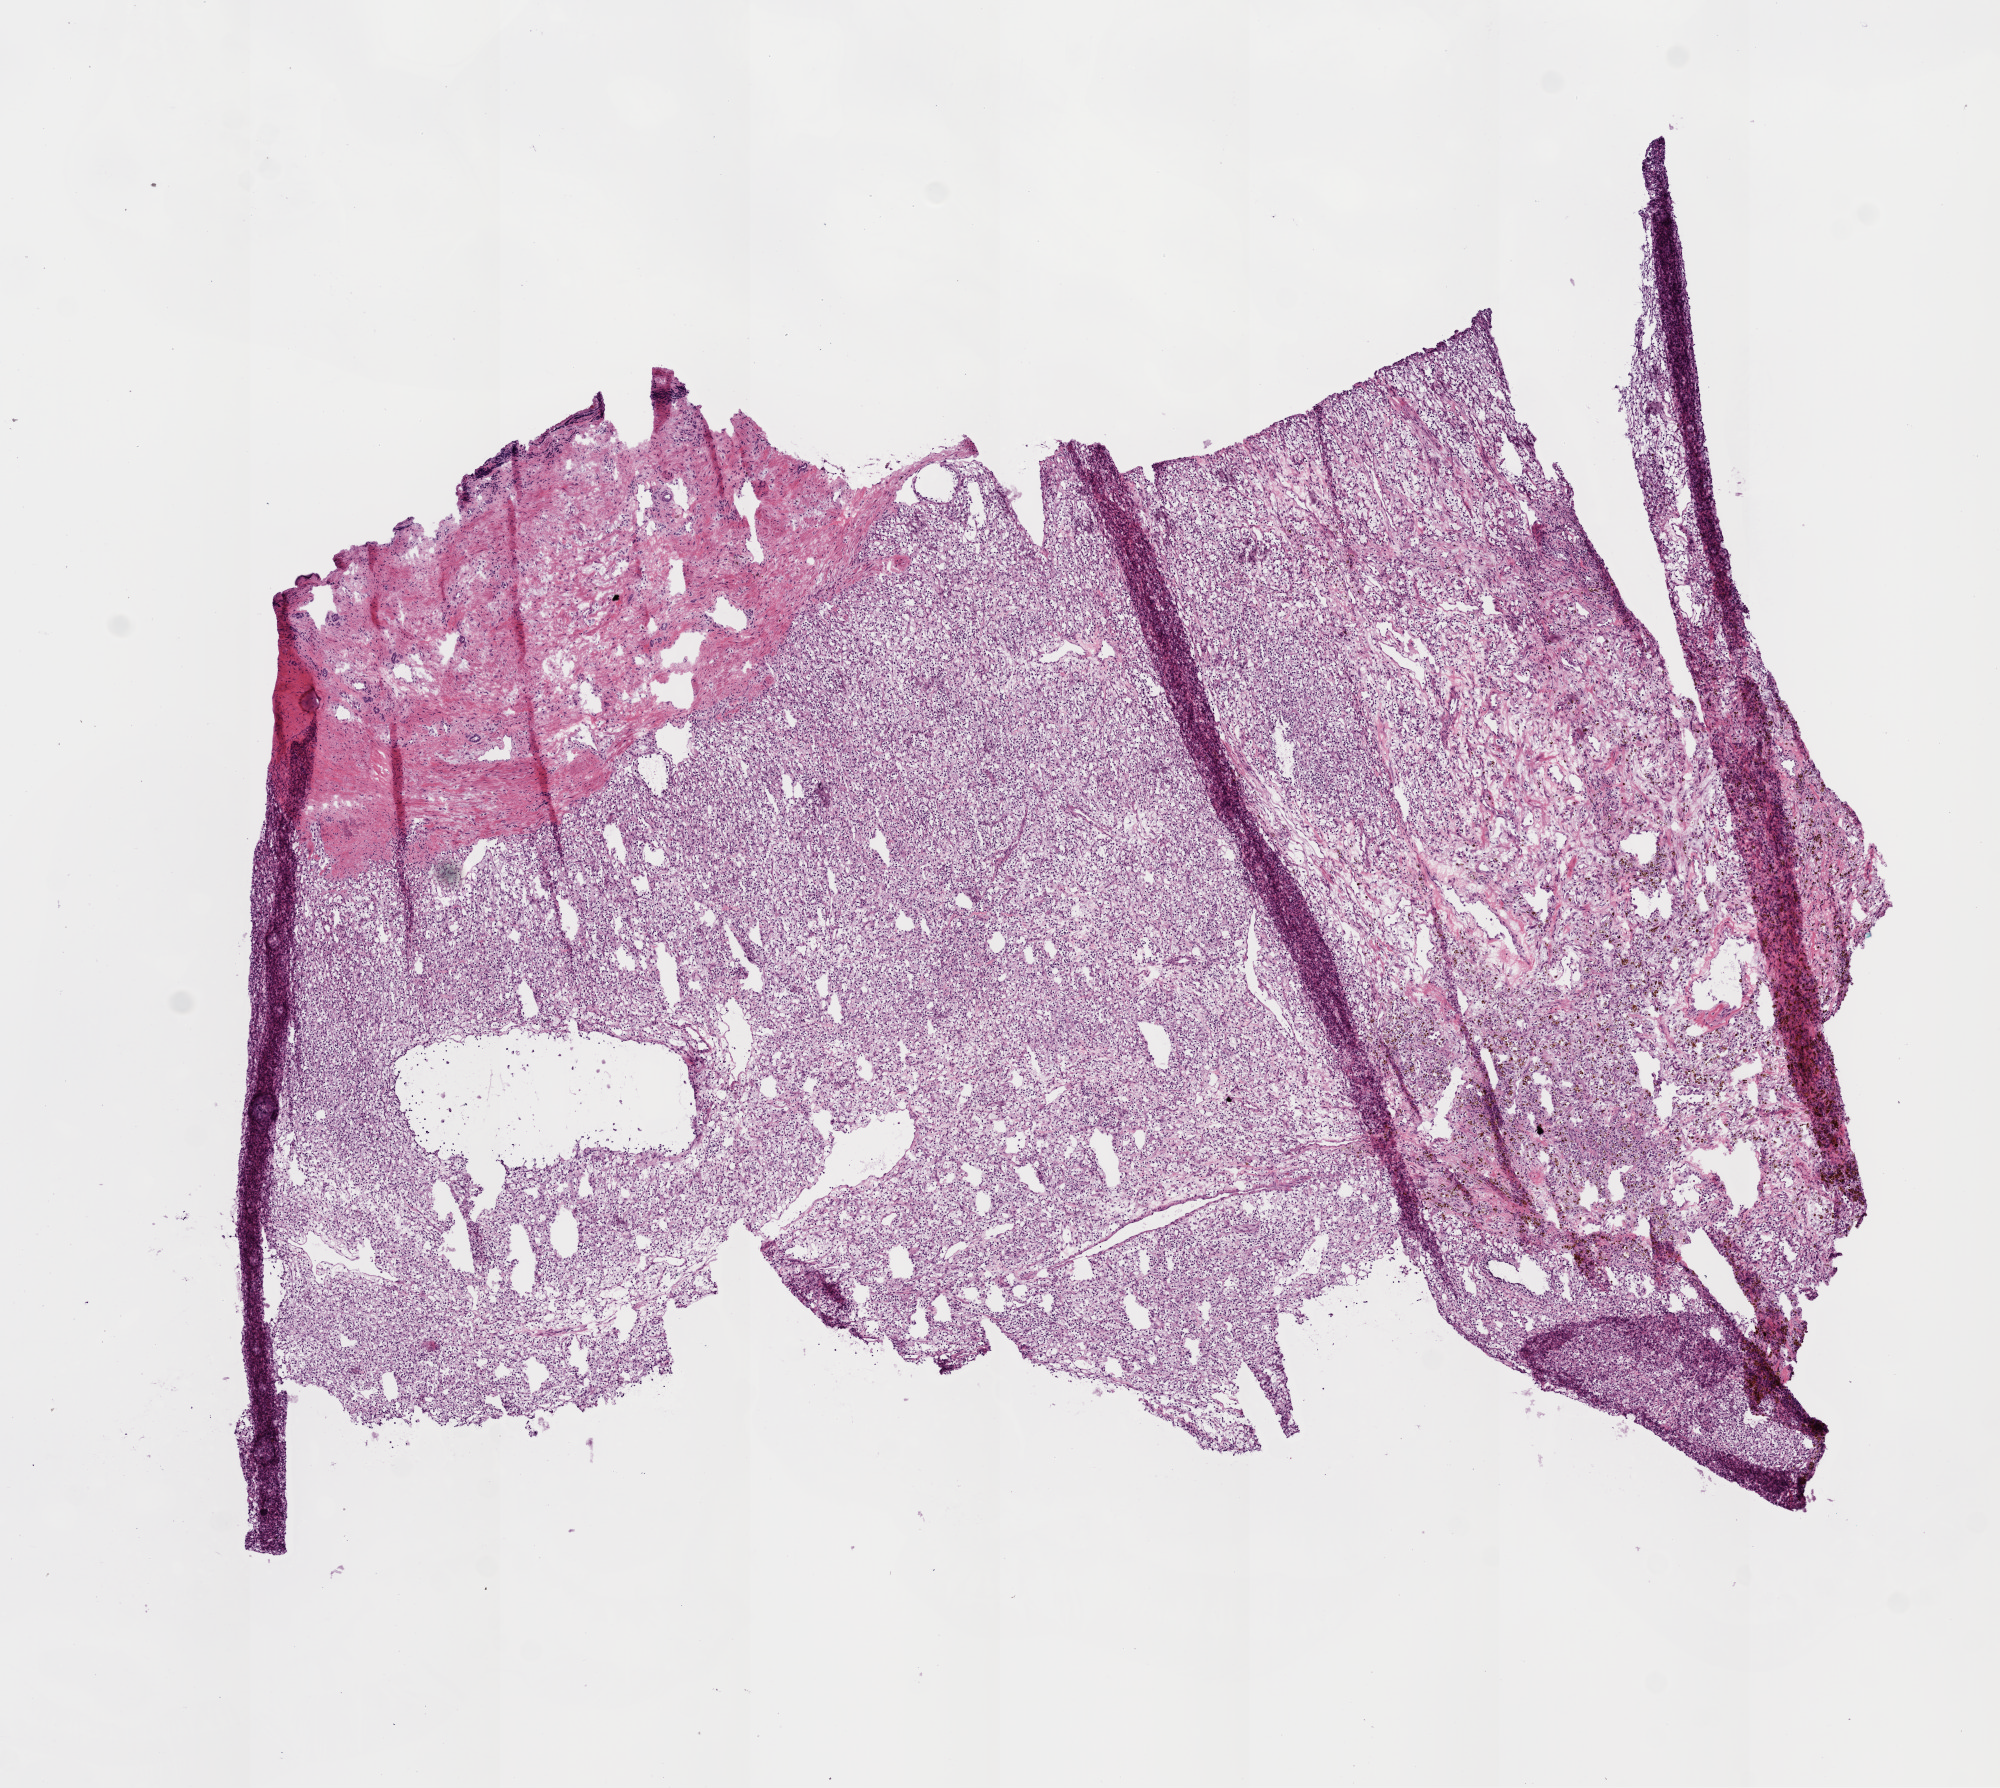
Whole-slide histology image, H&E-stained — a low-resolution overview of the entire scanned area, about 8.0 x 7.2 mm, frozen section, sample: primary tumour, kidney. Patient: male, age at initial diagnosis 52 years. Histologic grade: G2 (moderately differentiated). Pathologist review of this section (percent, as recorded): tumour cells 80%, tumour nuclei 85%, normal cells 12%, stromal cells 8%, necrosis 0%. Infiltration values recorded for this section: lymphocyte infiltration 3%, monocyte infiltration 3%, neutrophil infiltration 0%.
Diagnosis: Clear cell adenocarcinoma, NOS. Laterality: left. AJCC pathologic stage: I.